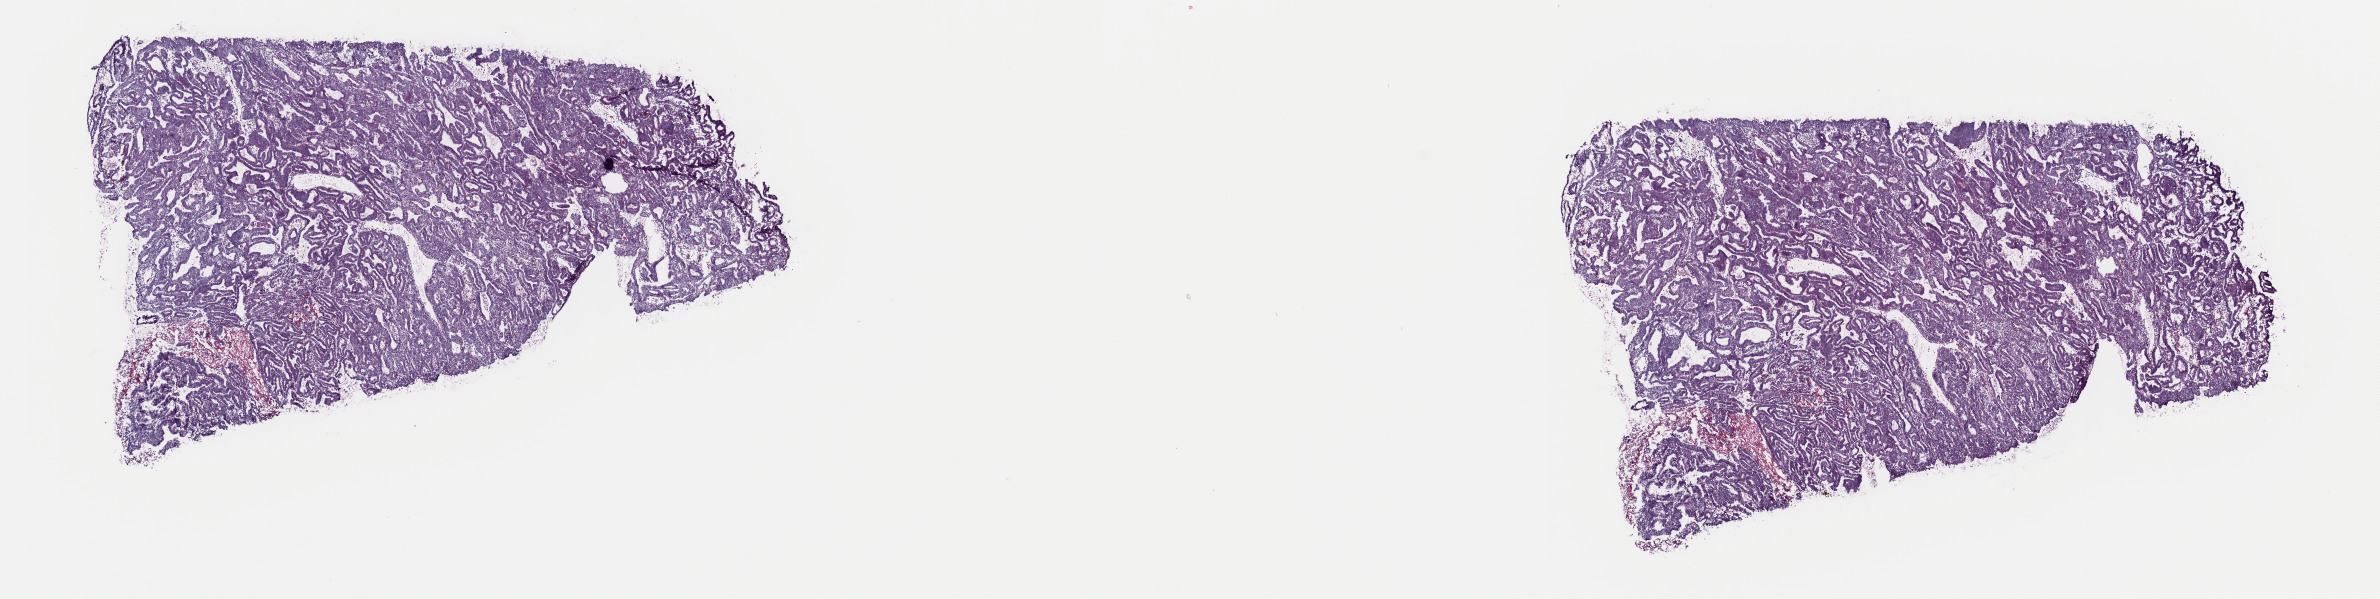
Whole-slide histology image, Hematoxylin and eosin (H&E) stained, shown as a low-resolution overview of the whole scanned area (about 18.8 x 4.7 mm), frozen section from the top of the tissue portion, sample: primary tumour, uterus. Patient: female, age at initial diagnosis 57 years. Histologic grade: G2 (moderately differentiated). Slide review estimates, as recorded: tumour cells 90%, tumour nuclei 90%, normal cells 0%, stromal cells 10%, necrosis 0%. Infiltration values recorded for this section: lymphocyte infiltration 1%, monocyte infiltration 1%, neutrophil infiltration 1%.
Histologic diagnosis: Endometrioid adenocarcinoma, NOS (endometrium). FIGO stage: II.